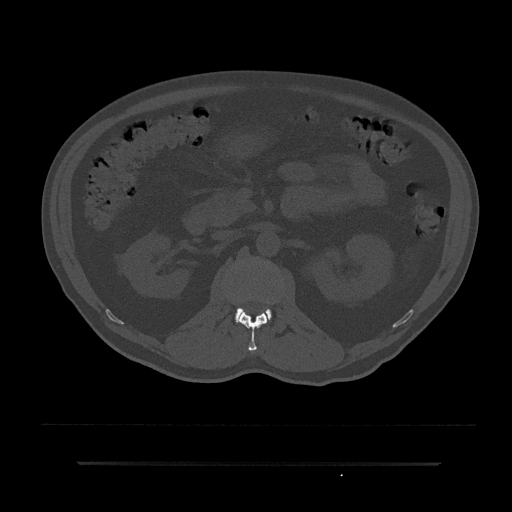
CT including the spine, one axial slice. Position 113 of 797 along the scan axis. Reconstruction kernel Br40s/3. 120 kVp. Bone window (W 1800 / L 400 HU). 0.5 mm slice thickness. 512 × 512 image matrix, field of view 464 × 464 mm. Patient: male, 59 years. Case-level facts recorded for this patient, not image findings: primary cancer: bile ducts; vertebrae with lytic lesions (as recorded): T10.
Structures marked on this image (semi-automatically segmented with operator editing):
- L1 vertebra: bounding box (x1, y1, x2, y2) in pixels: (238, 310, 269, 354)
- L2 vertebra: (235, 308, 272, 322)